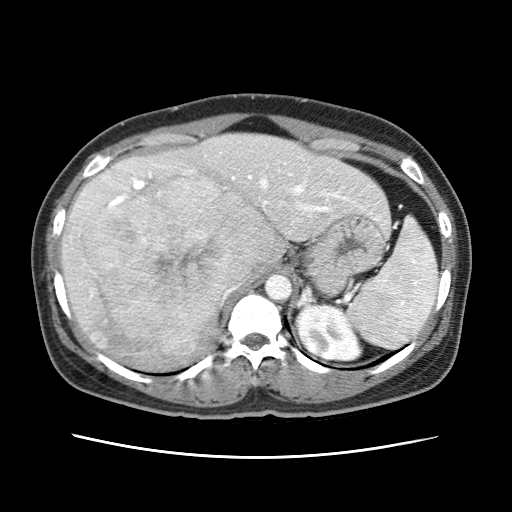
Contrast-enhanced abdominal CT (liver protocol), one axial slice. Slice 44 of 79 in the series (ordered by position). Soft-tissue window (W 400 / L 40 HU). 2.5 mm slice thickness. 512 × 512 image matrix, field of view 340 × 340 mm. From the clinical record (not read from this slice): diagnosis: hepatocellular carcinoma (patient treated with transarterial chemoembolisation; whether this scan precedes or follows treatment is not stated here); TNM stage (as recorded): Stage-I; Child-Pugh class: A; tumour differentiation: moderately differentiated.
Annotated regions visible in this slice (semi-automatic segmentation, software-assisted and operator-edited):
- abdominal aorta: bounding box (x1, y1, x2, y2) in pixels: (266, 274, 294, 300)
- liver parenchyma outside the tumour (the mass and vessels are separate outlines, so this box may not span the whole liver): (60, 134, 383, 366)
- mass: (85, 177, 282, 352)
- liver vessels: (77, 170, 348, 212)